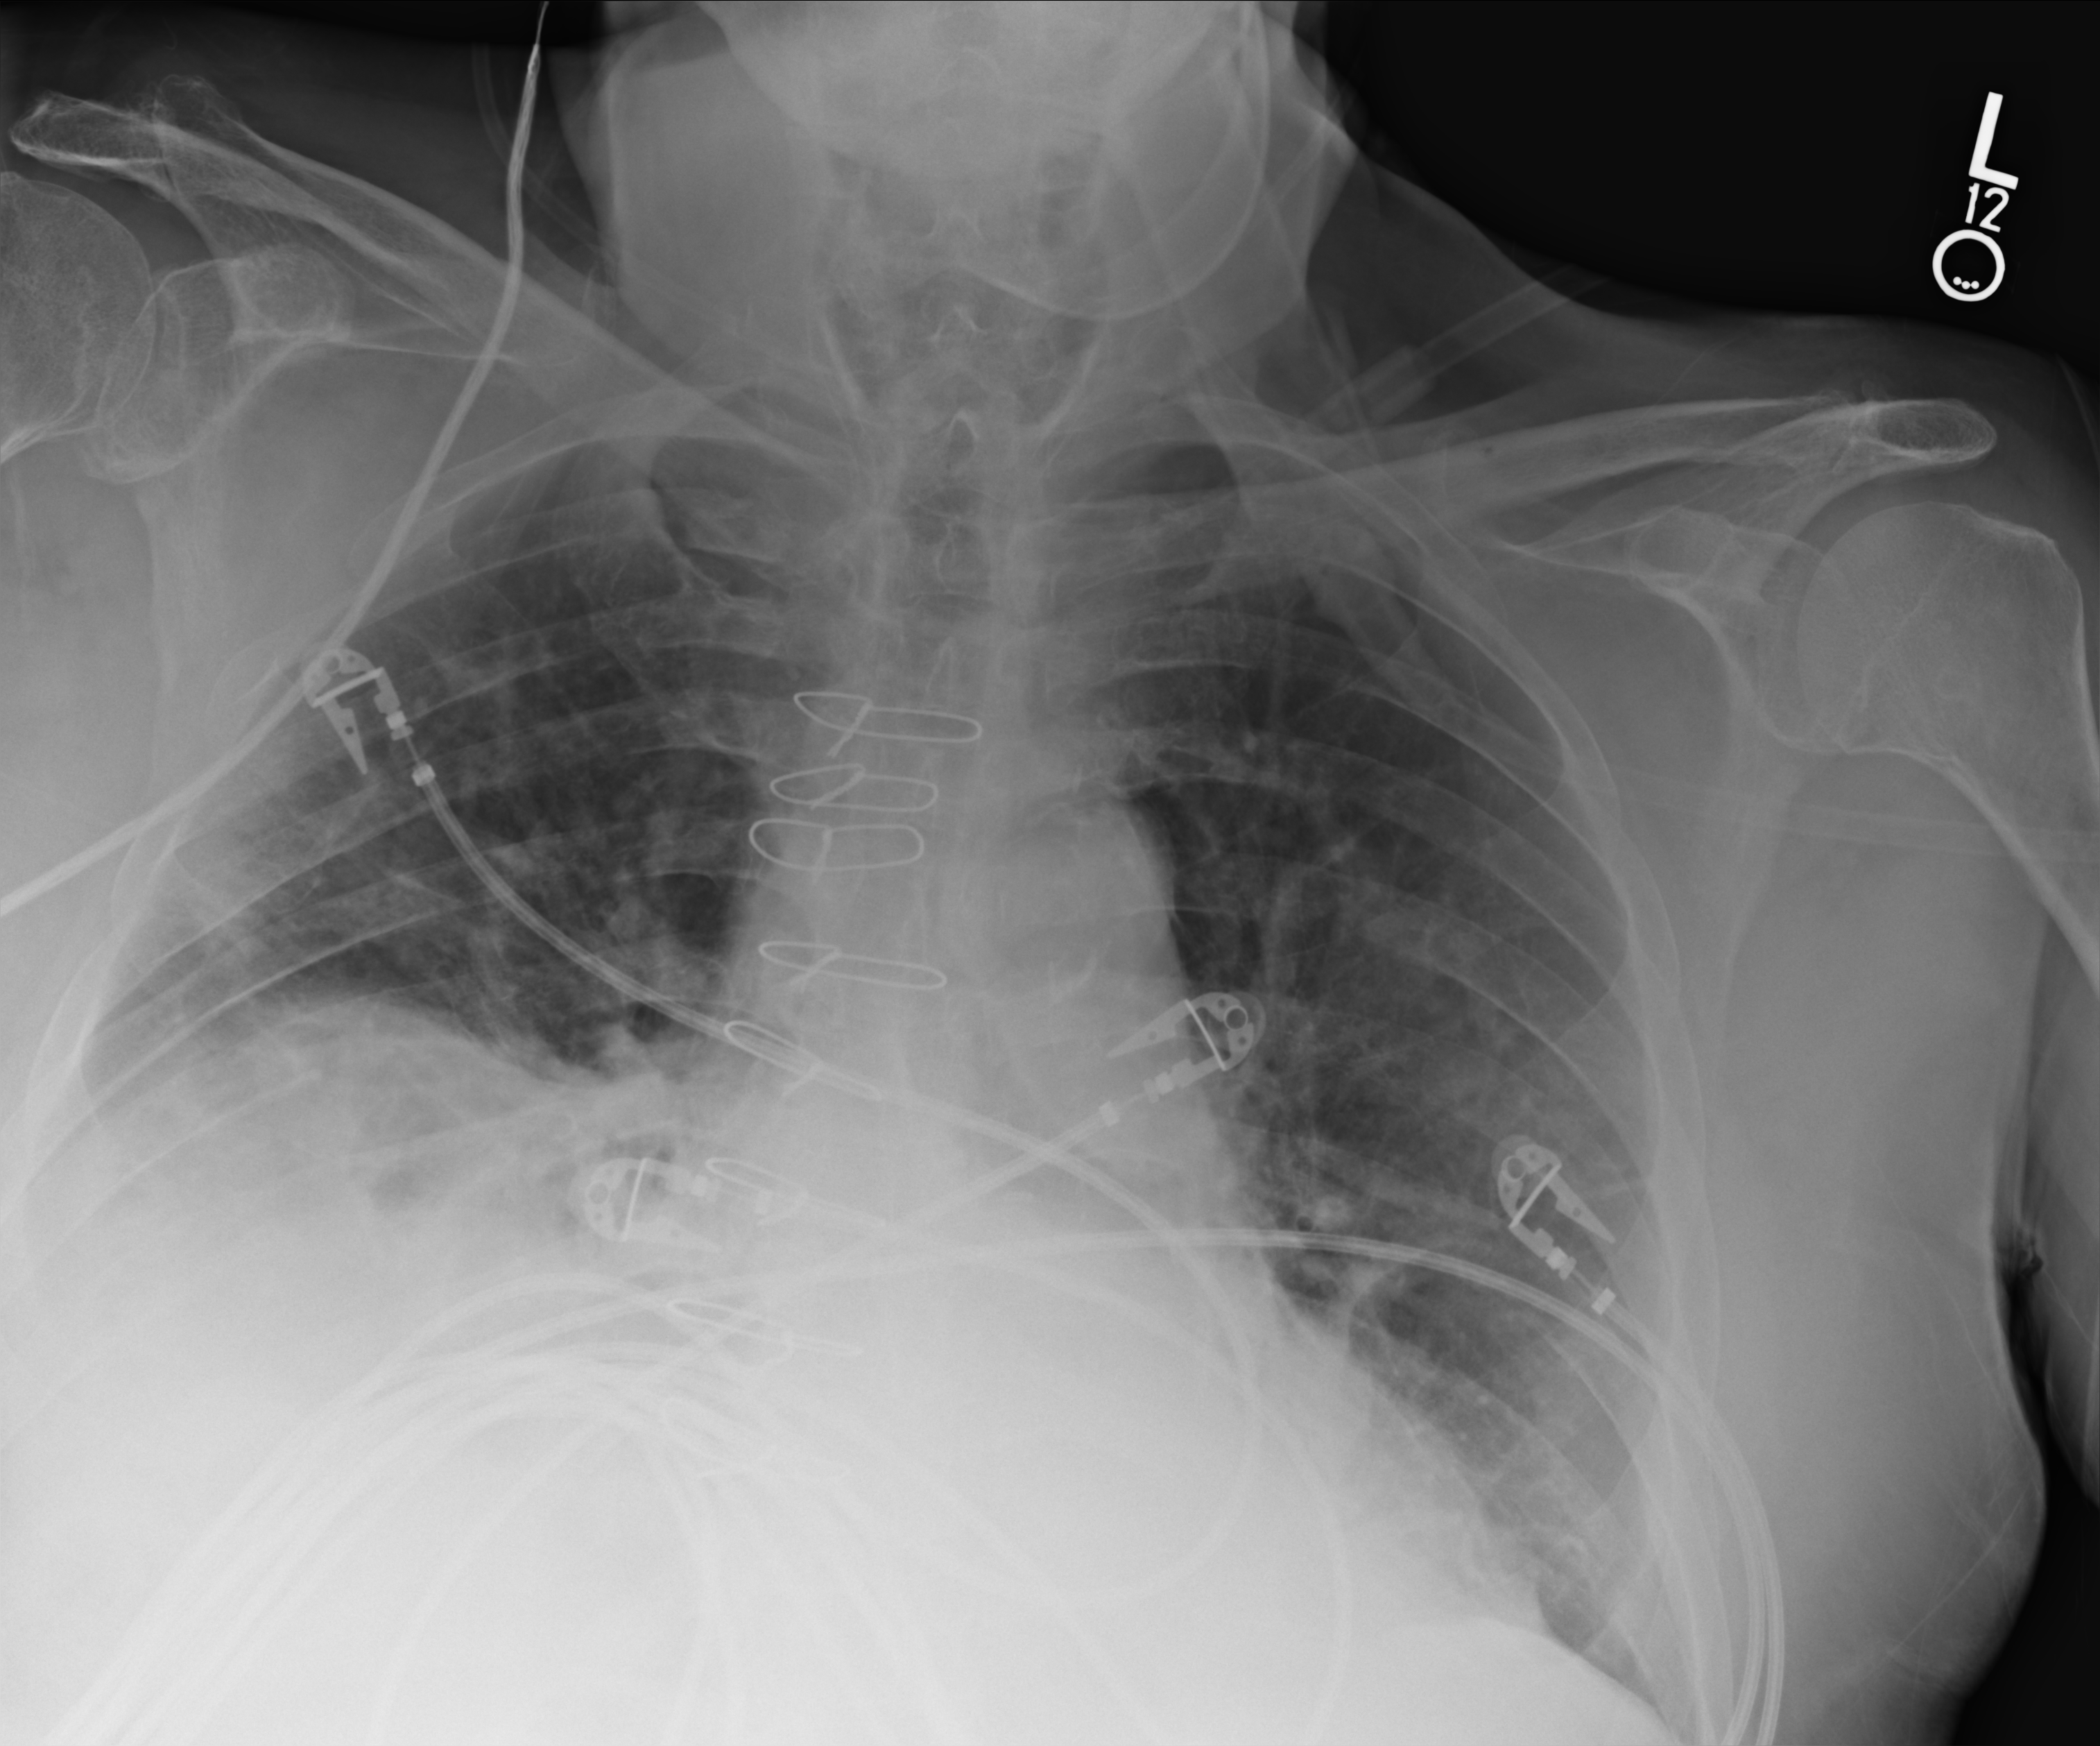
Chest X-ray (portable). Male patient hospitalised with COVID-19, age 75–90 years.
Hospital-stay facts (about this admission, not read from this image; timing relative to this image not recorded): admitted to intensive care during this hospital stay: no.